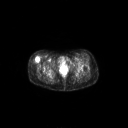
FDG PET of an extremity soft-tissue mass (from a PET/CT study), one axial slice. Slice 54 of 267 in the series (ordered by position). 128 × 128 image matrix, field of view 700 × 700 mm. Patient: female, 34 years. Case-level facts recorded for this patient, not image findings: histological type: synovial sarcoma; grade: intermediate; site of the primary tumour: right thigh.
Annotated regions visible in this slice (expert contour drawn on MRI and transferred to this co-registered scan by the dataset authors):
- gross tumour volume including surrounding oedema: bounding box [x1, y1, x2, y2] px = [34, 56, 39, 62]
- gross tumour volume (mass): [34, 56, 39, 62]